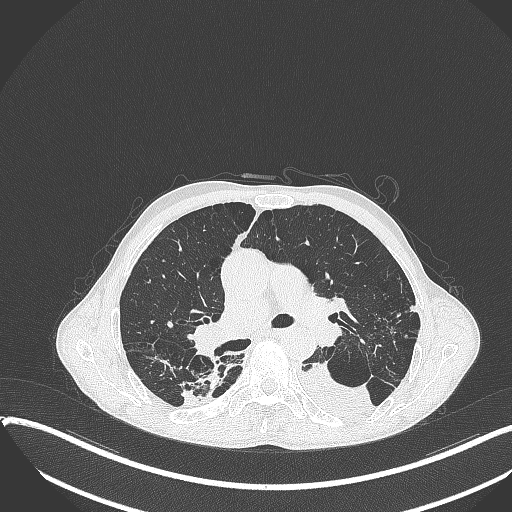
Chest CT, one axial slice; position 234 of 401 along the scan axis; 120 kVp; lung window (W 1500 / L -600 HU); 1 mm slice thickness; 512 × 512 image matrix. Male patient, age 57 years. From the clinical record (not read from this slice): clinical TNM (as recorded): T4 N0 M0.
Structures marked on this image (bounding box drawn by a radiologist):
- lung tumour (recorded histology: squamous cell carcinoma): bounding box <298,357,376,421> (left, top, right, bottom; pixels)